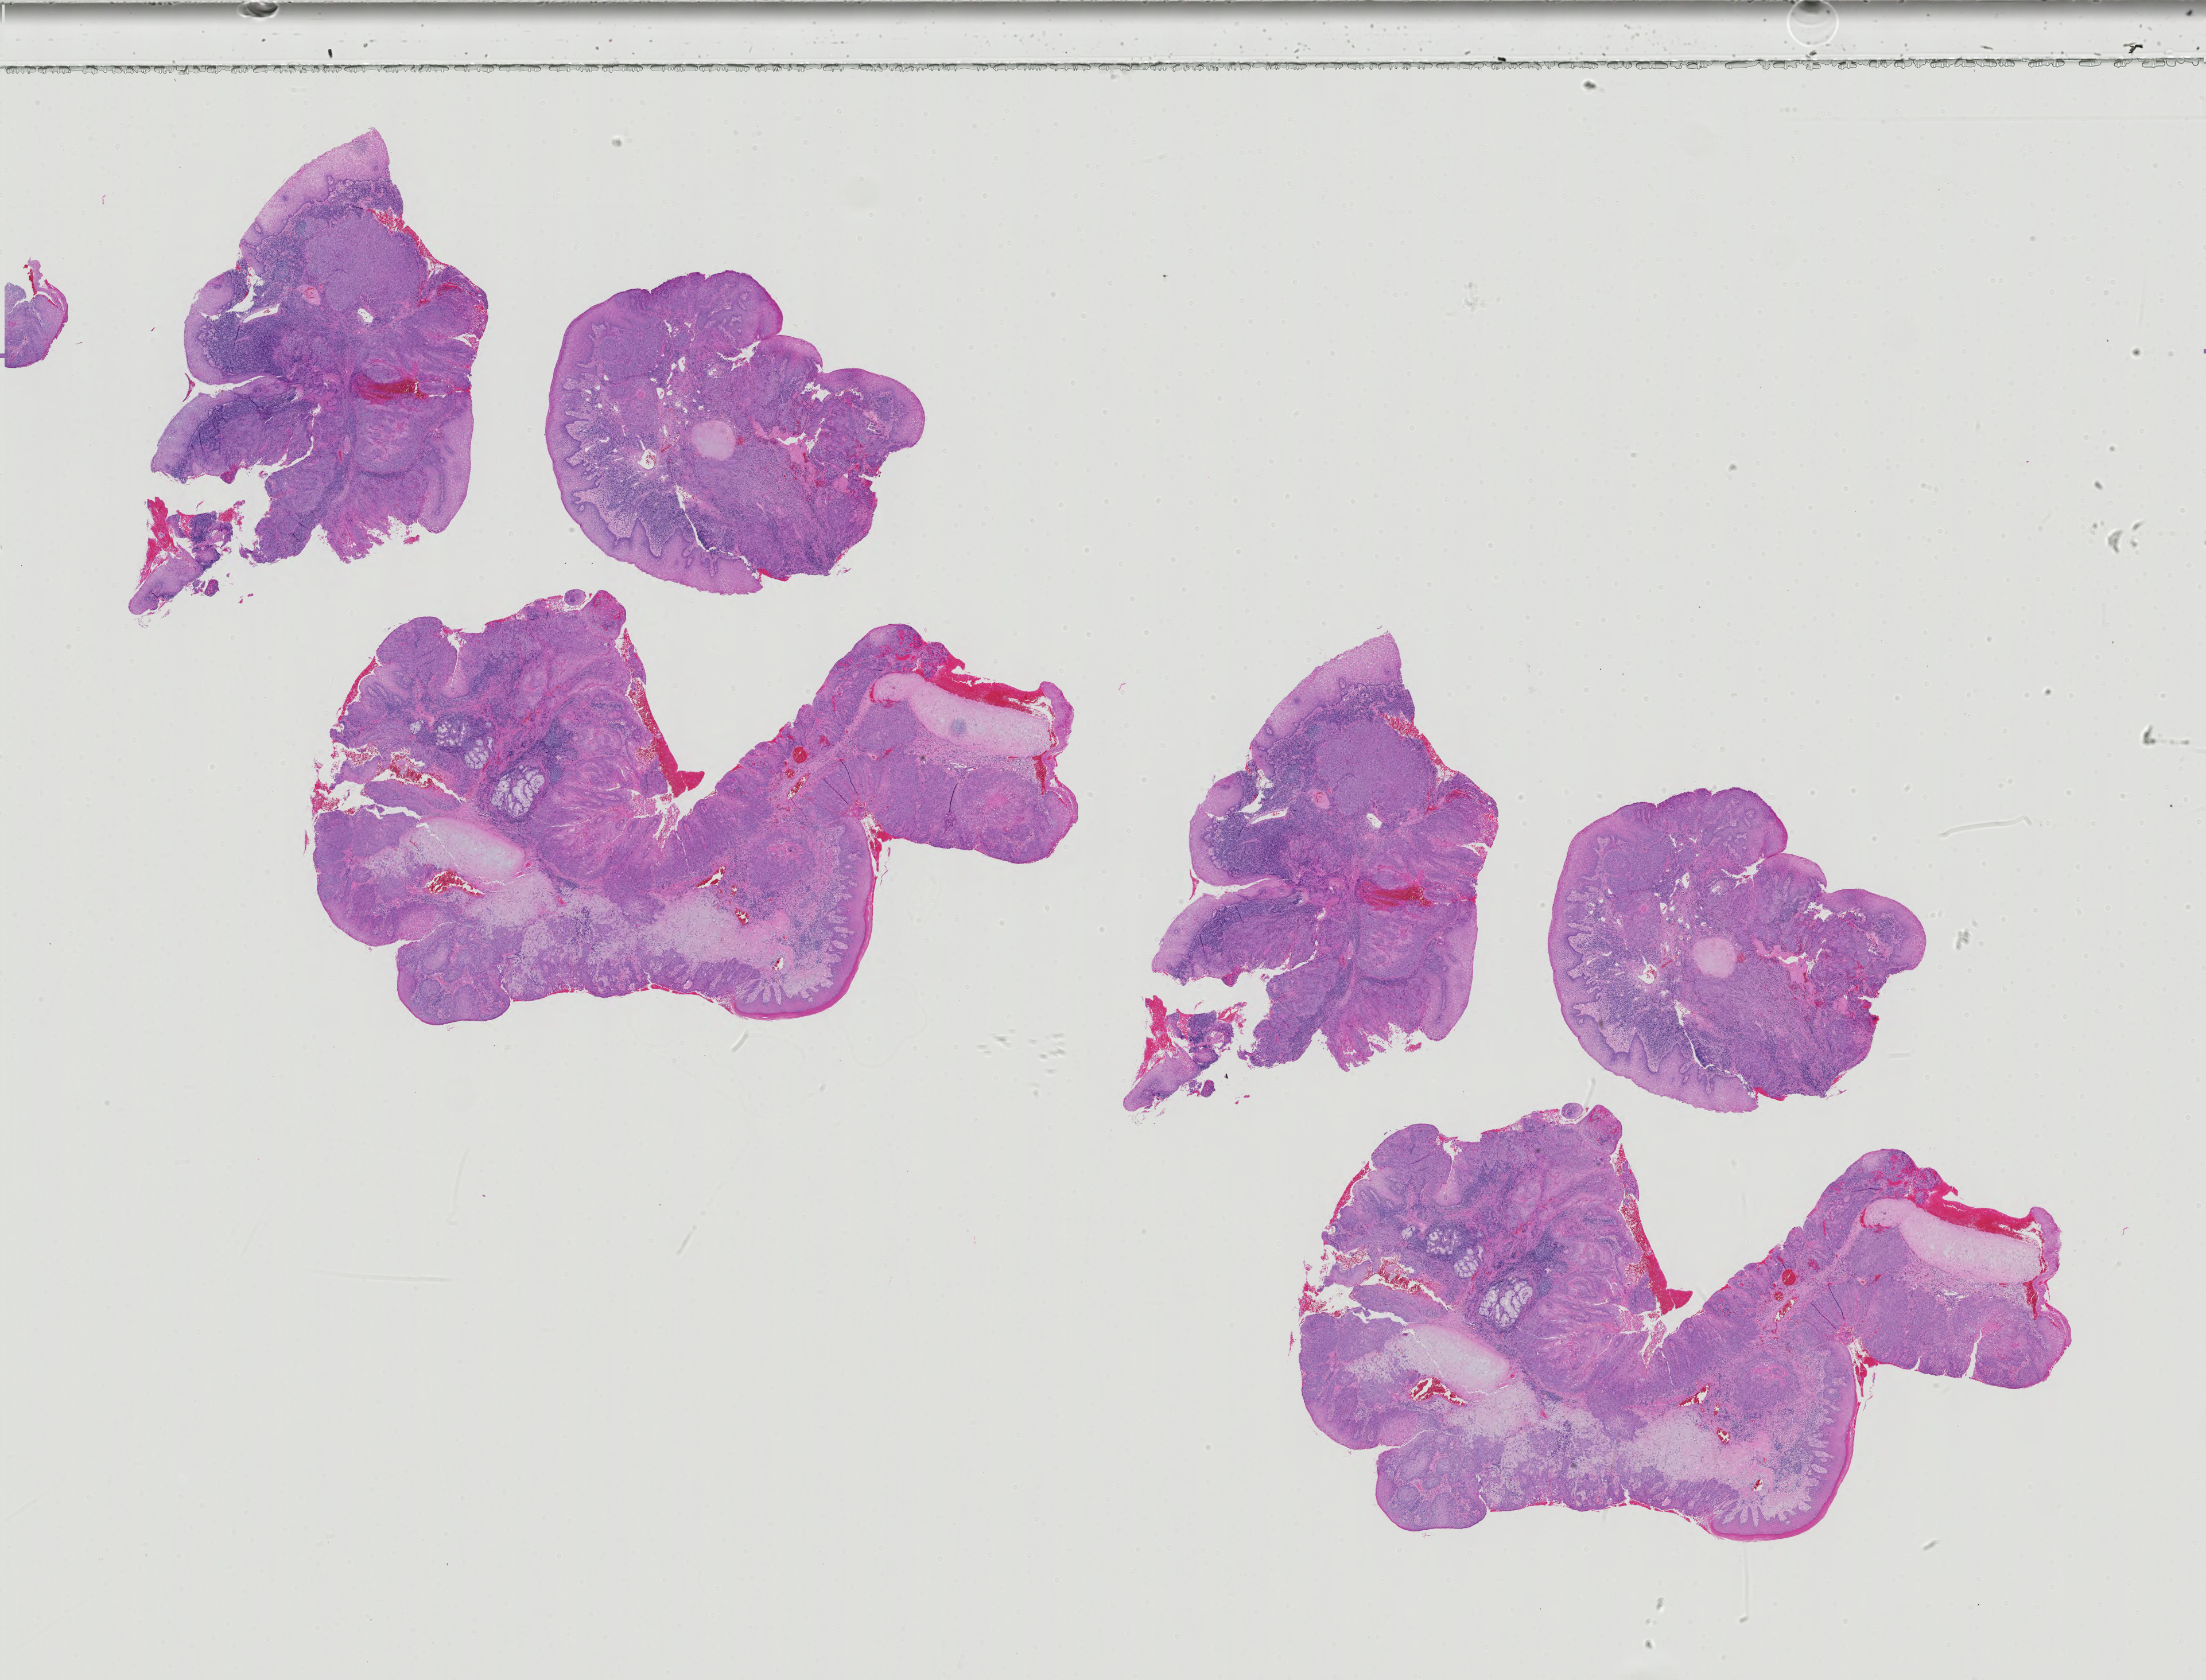
Digitized Hematoxylin and eosin (H&E) stained tissue section (whole slide), shown as a low-resolution overview of the whole scanned area (about 27.9 x 21.2 mm, acquisition: 40x scan). Formalin-fixed paraffin-embedded (FFPE) diagnostic section. Primary tumour sample from the head and neck. Female, age 60 years at initial diagnosis. Histologic grade: G2 (moderately differentiated).
TNM: T3 N1 M1. Histologic diagnosis: Squamous cell carcinoma, NOS (larynx, NOS). AJCC pathologic stage: IVC (7th edition). Laterality: left.